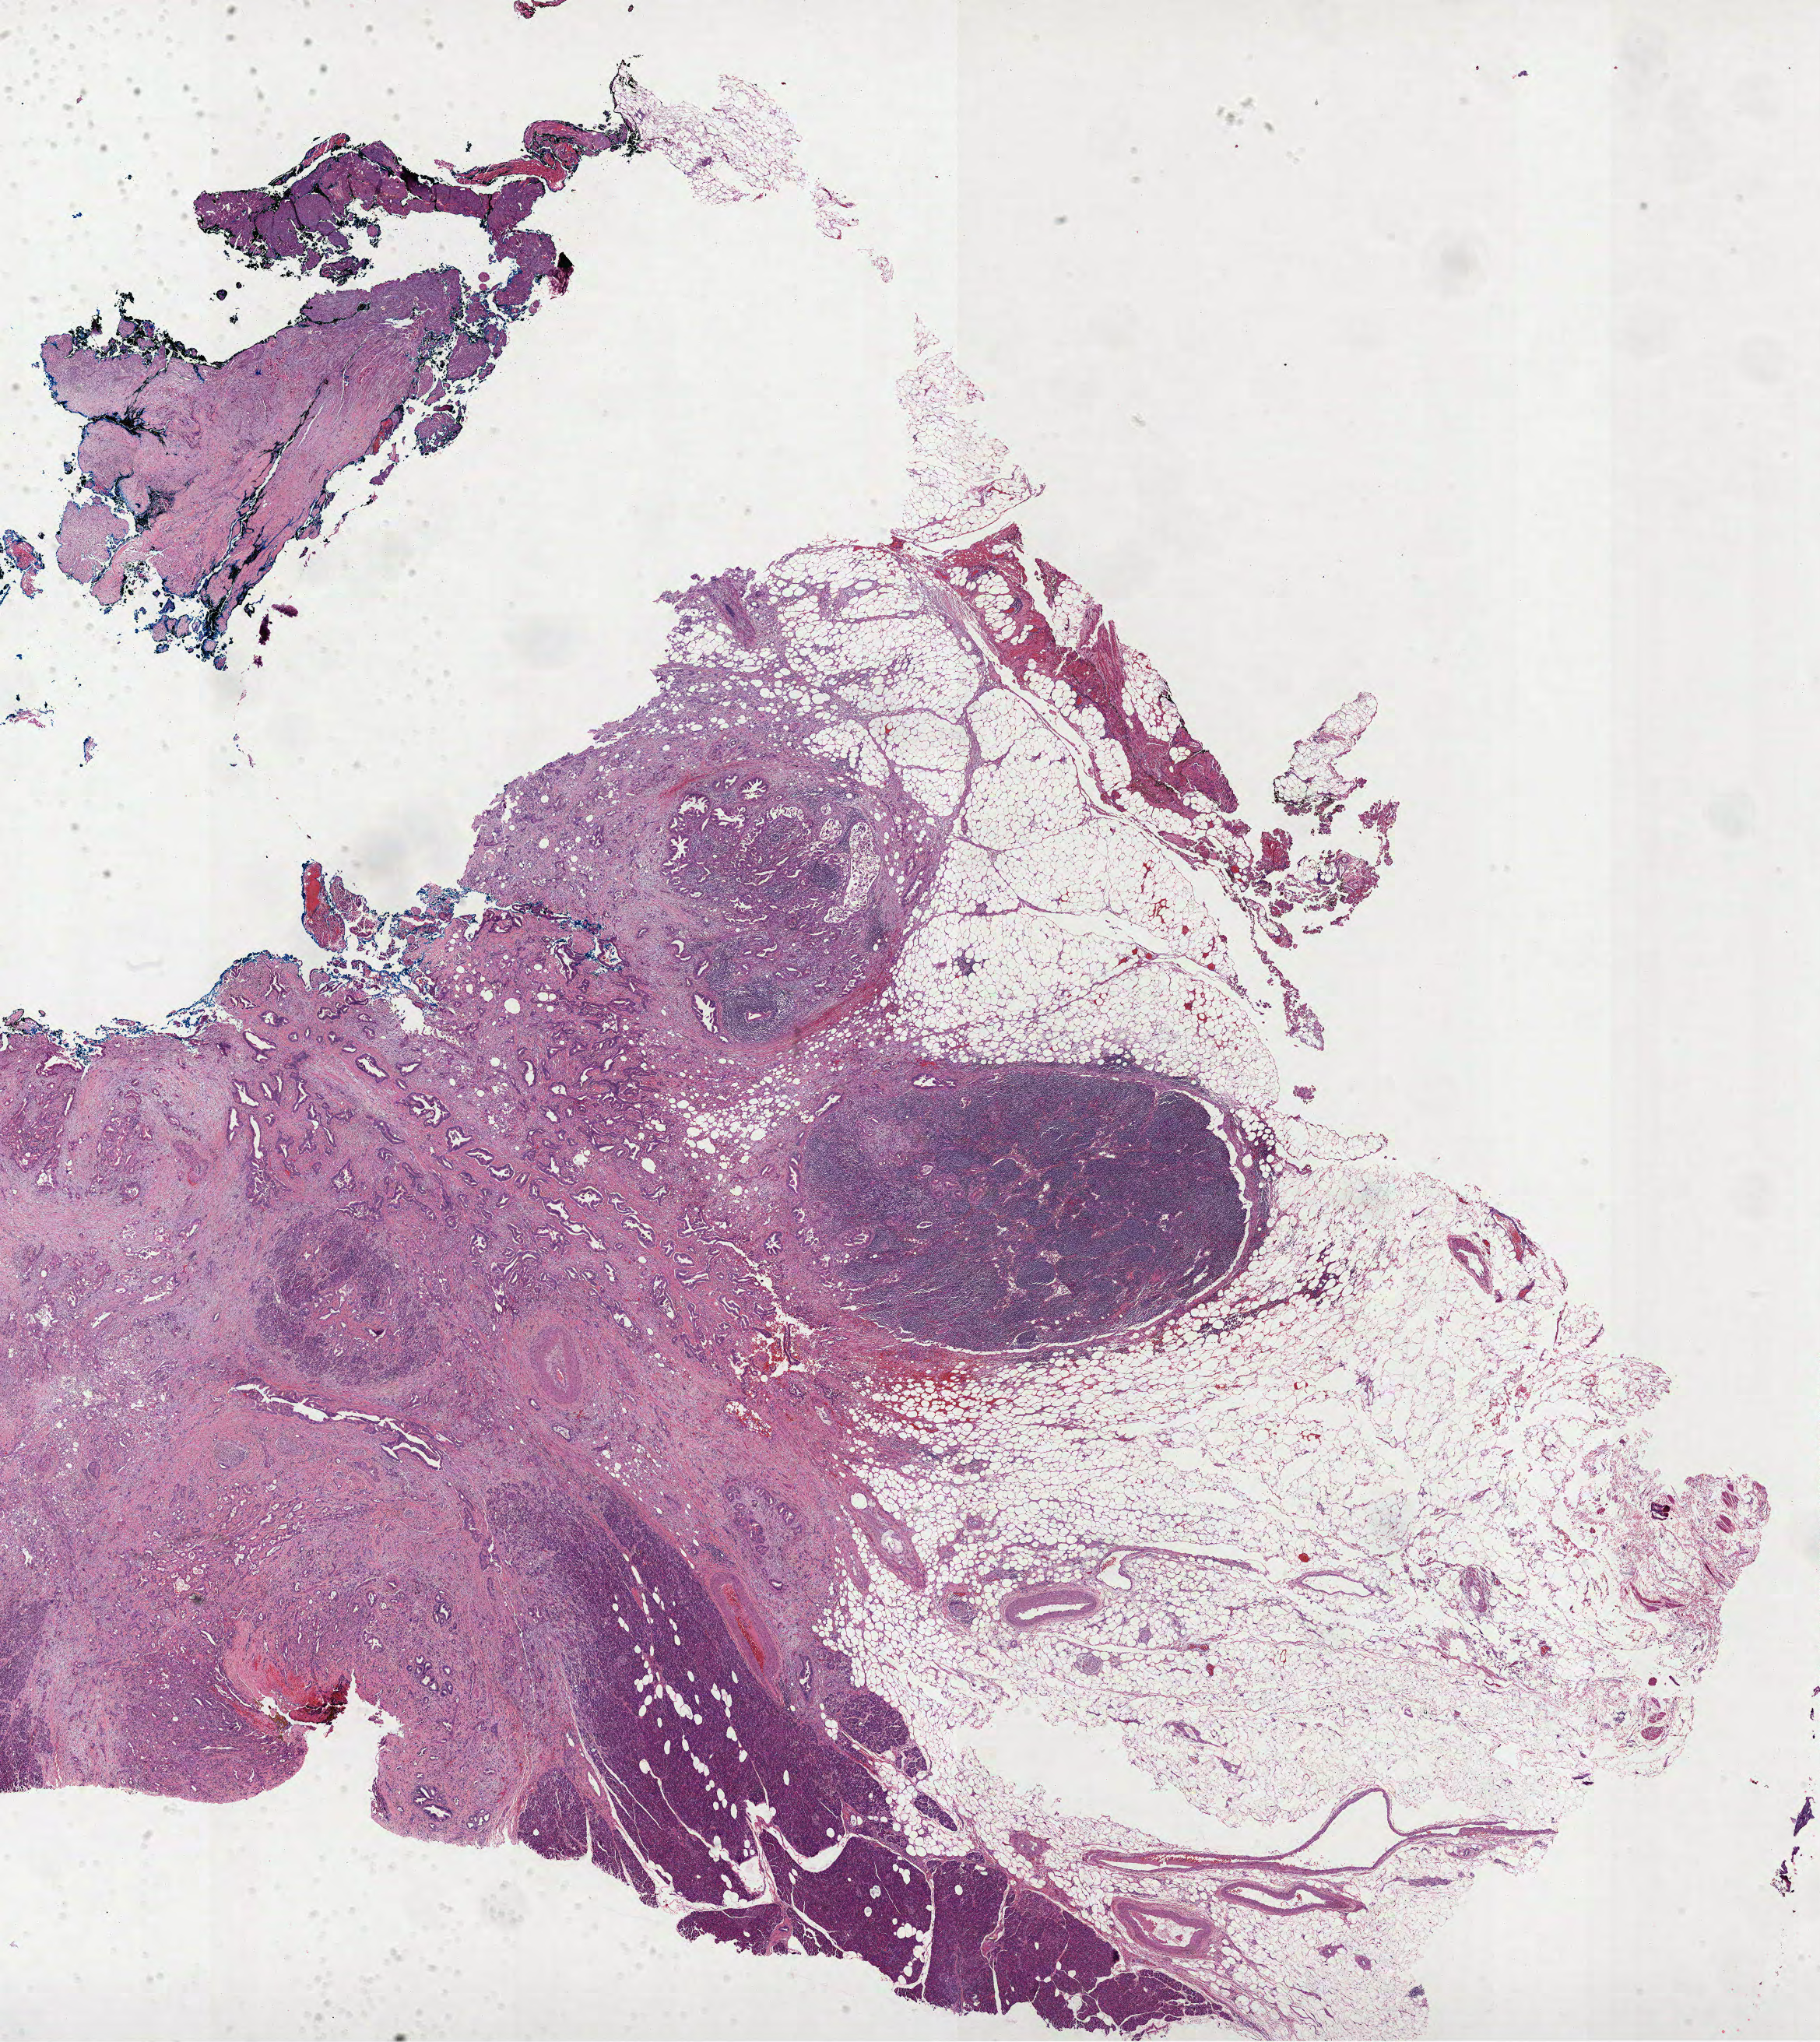
Digitized H&E tissue section (whole slide) — whole scanned area (about 18.9 x 21.2 mm) shown as a low-resolution overview; formalin-fixed paraffin-embedded (FFPE) diagnostic section; sample: primary tumour, pancreas. Male, age 52 years at initial diagnosis. Histologic grade: G3 (poorly differentiated).
- AJCC pathologic stage: IIB (6th edition)
- pathologic diagnosis: Infiltrating duct carcinoma, NOS (head of pancreas)
- TNM: T3 N1 M0
- lymph nodes positive (case pathology): 3 of 9 examined